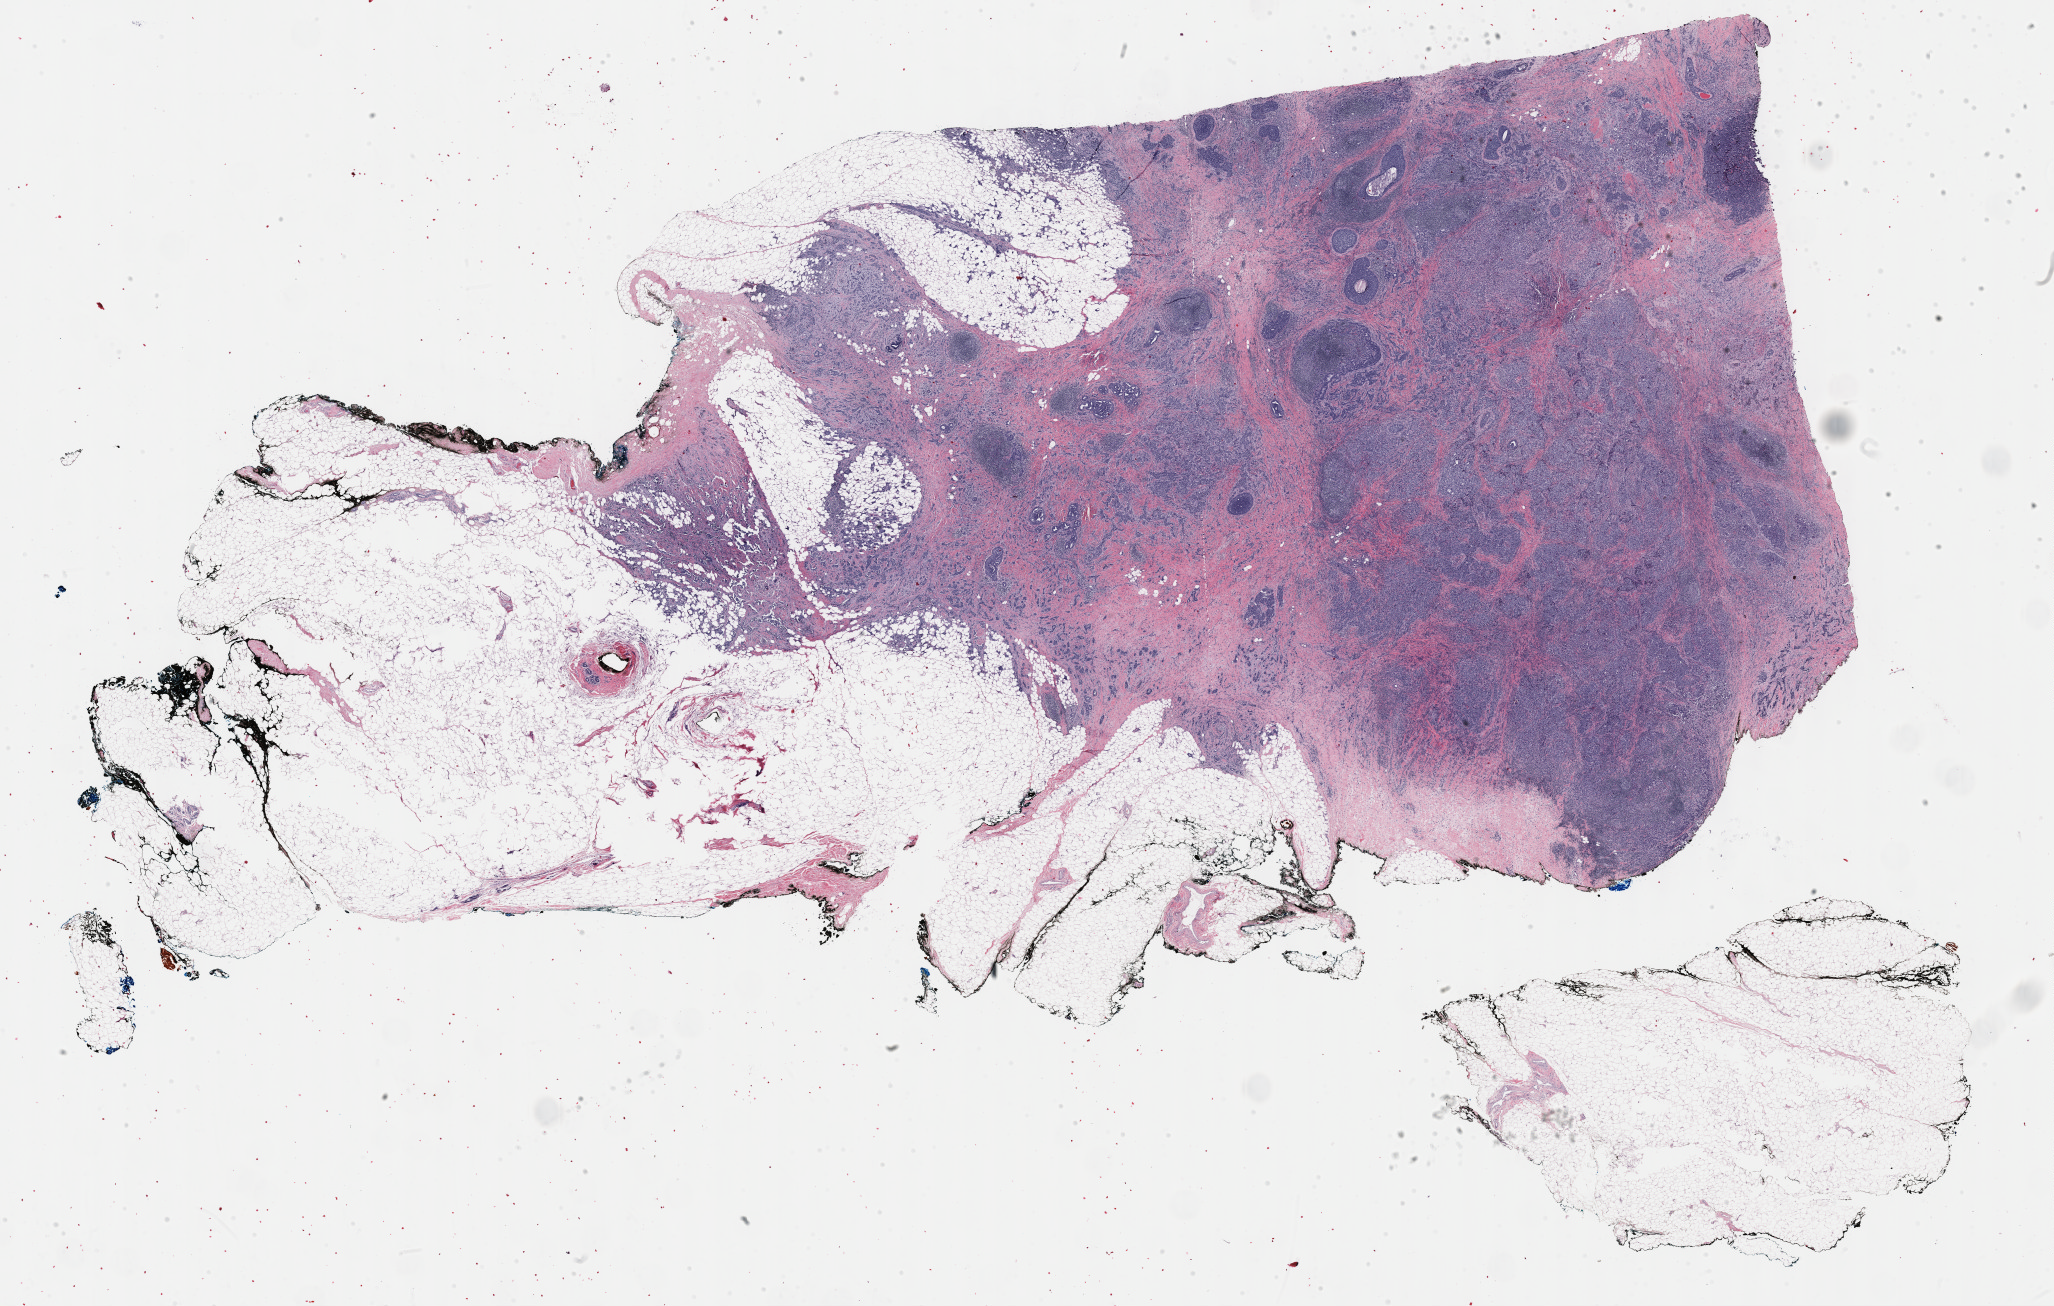
Digitized Hematoxylin and eosin (H&E) stained tissue section (whole slide), shown as a low-resolution overview of the whole scanned area (about 33.2 x 21.1 mm, from a 40x scan); formalin-fixed paraffin-embedded (FFPE) diagnostic section; sample: primary tumour, breast. Patient: female, age at initial diagnosis 52 years.
Laterality: left. Pathologic diagnosis: Infiltrating duct carcinoma, NOS. AJCC pathologic stage: IIIC (7th edition).